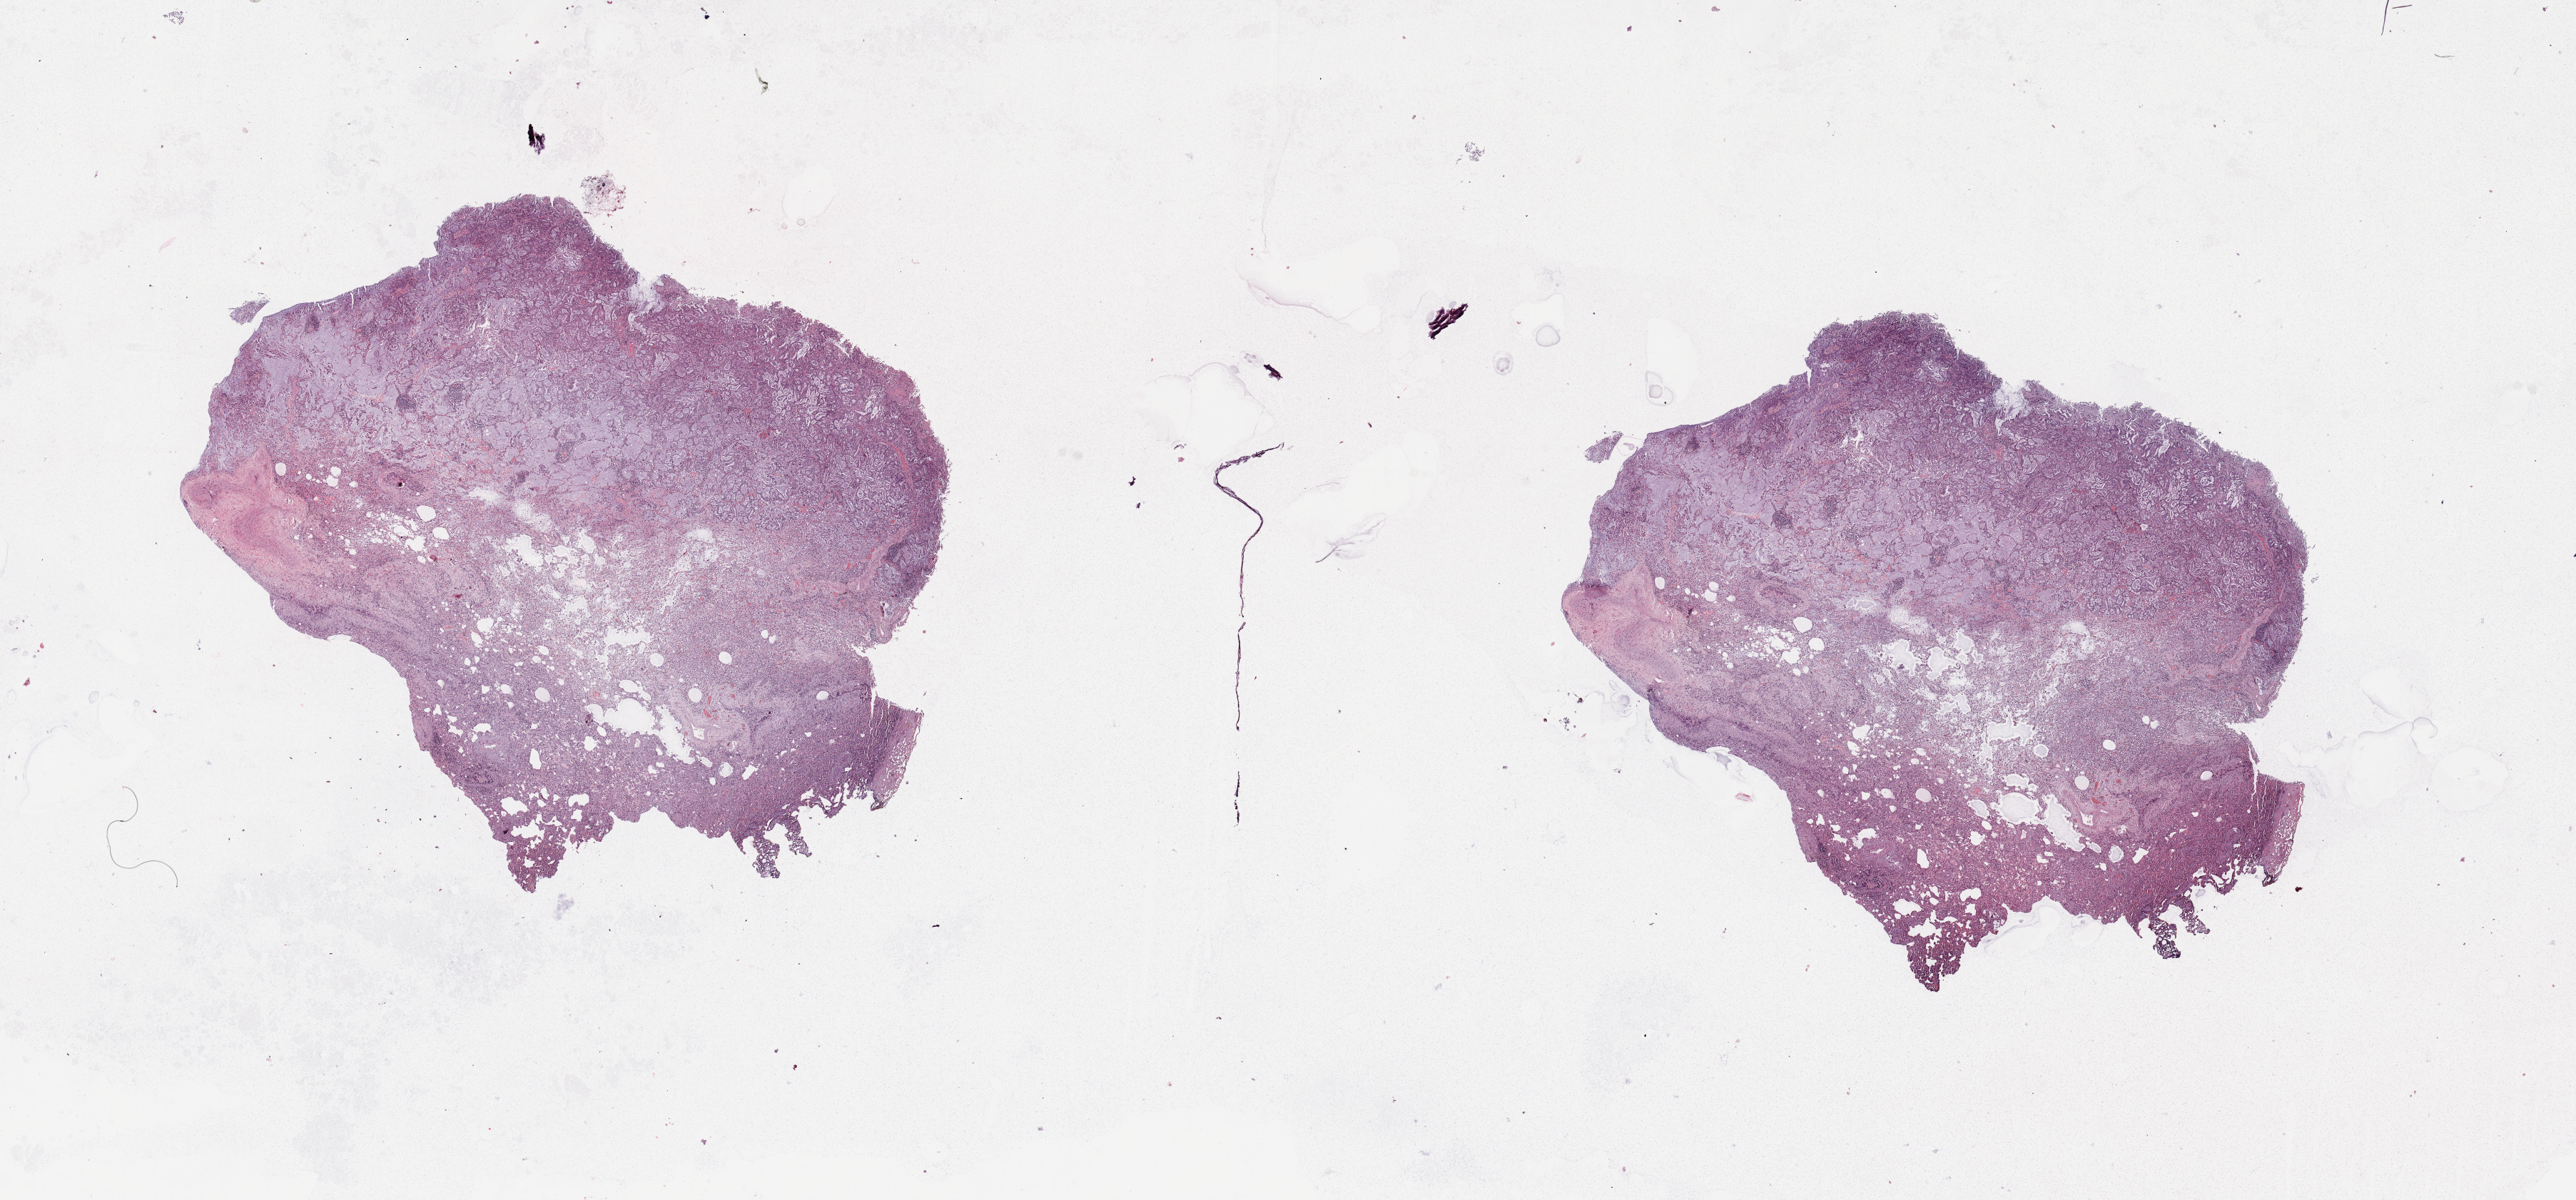
Whole-slide histology image, H&E — a low-resolution overview of the entire scanned area, about 28.5 x 13.3 mm, tumour tissue sample, sampled site: lung. Male, 67 y/o. Histologic grade: G2 (moderately differentiated). Composition of this section per pathologist review: tumour nuclei 65%, necrosis 10%.
- AJCC pathologic stage: IIA
- histologic diagnosis: Adenocarcinoma, NOS